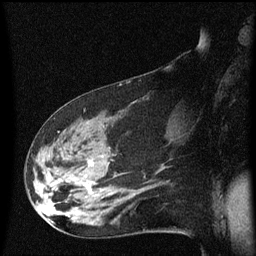
Breast MRI (dynamic contrast-enhanced), one sagittal slice. Position 32 of 60 along the scan axis. Dynamic contrast-enhanced series, image 2 of 3 at this slice position (ordered by acquisition). 1.5 T. TE 4.2 ms, TR 8.4 ms. 256 × 256 image matrix, field of view 200 × 200 mm. Female patient, age 48 years.
Annotated regions visible in this slice (semi-automatically segmented with operator editing):
- analysis volume of interest (the breast-tissue region the enhancement analysis was run in; not a lesion): bounding box <31,116,134,225> (left, top, right, bottom; pixels)
- tumour enhancement mask (voxels above the 70 % enhancement threshold inside the analysis volume of interest): <84,162,94,195>